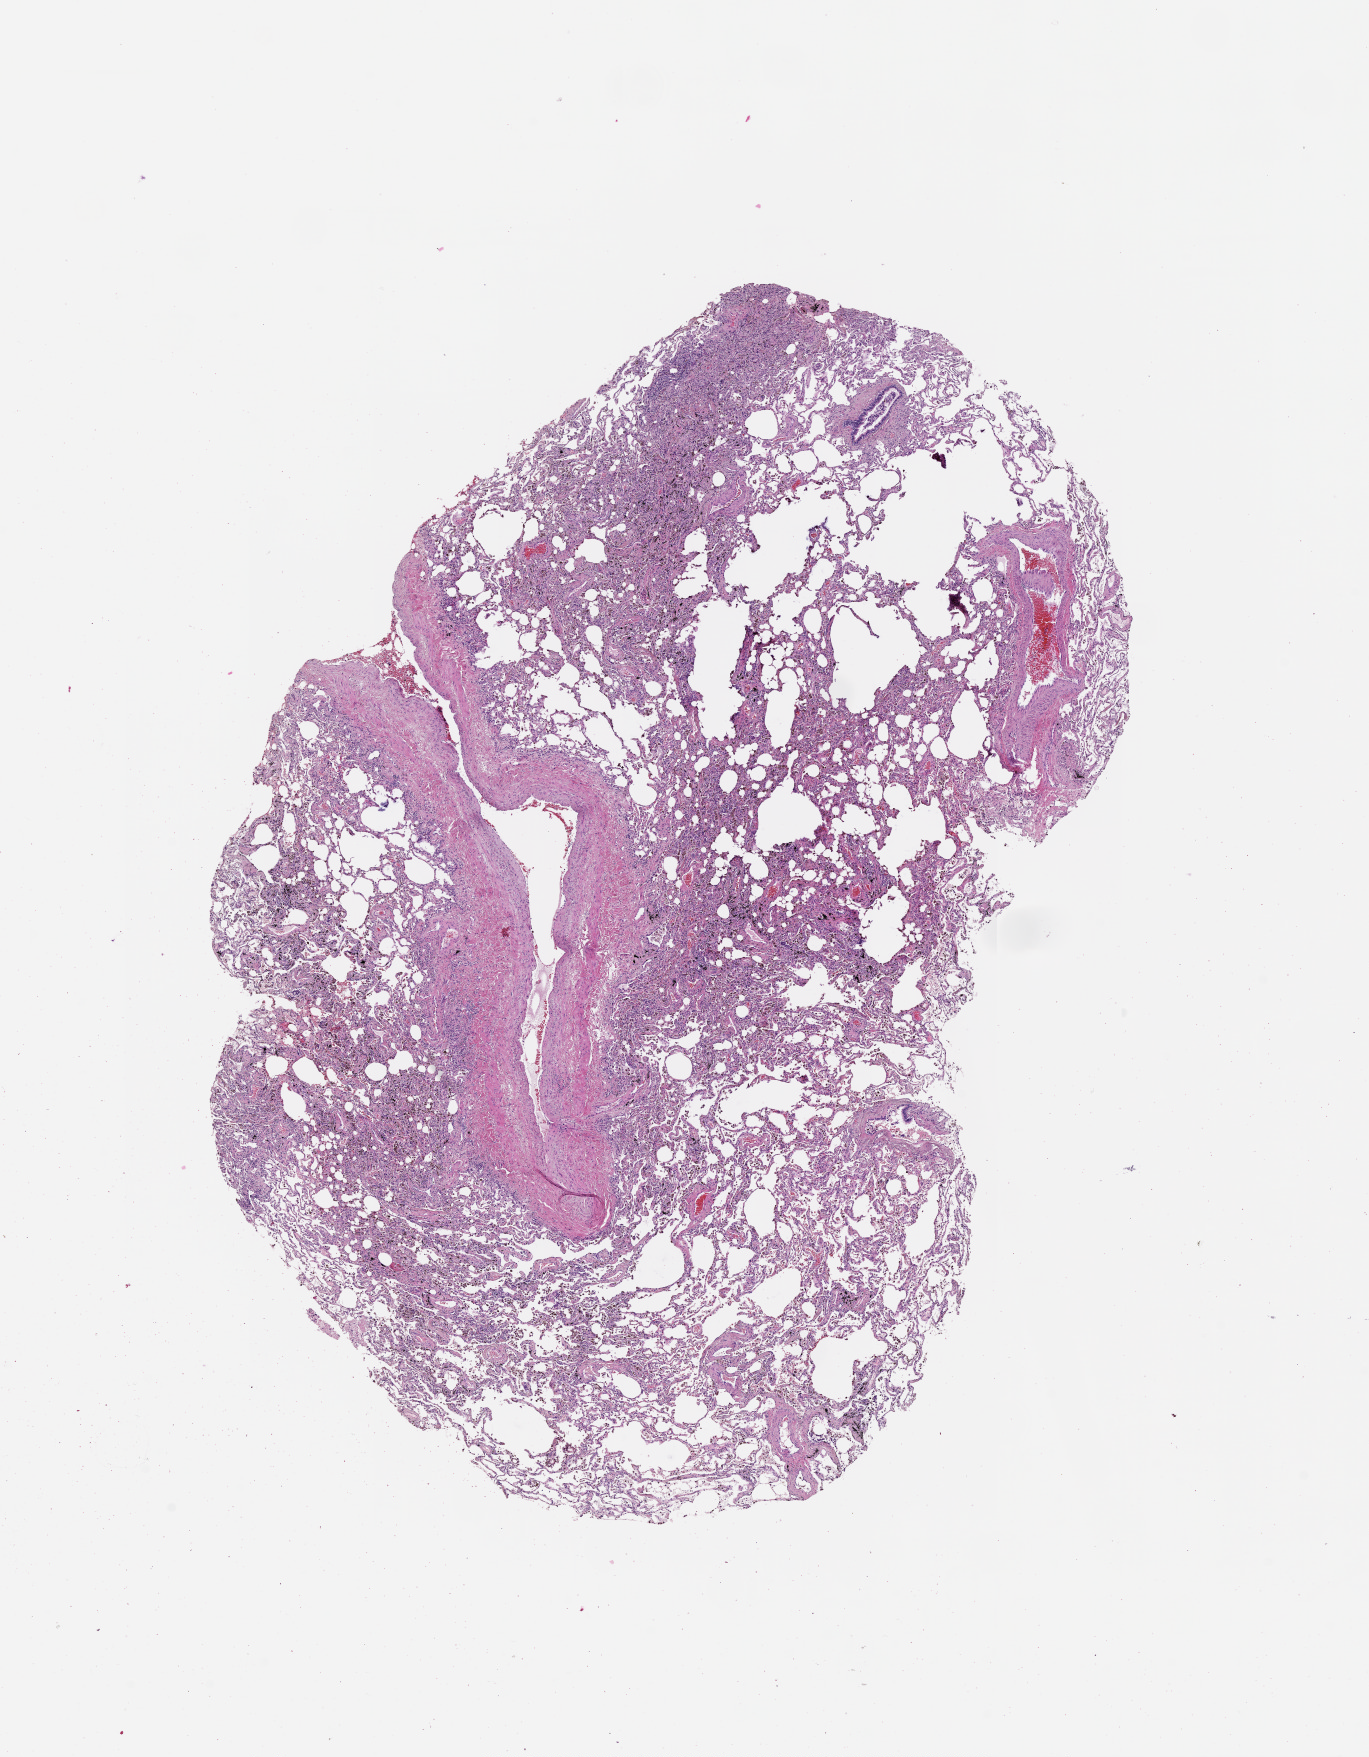
Whole-slide histology image, Hematoxylin and eosin (H&E) stained — a low-resolution overview of the entire scanned area, about 11.0 x 14.1 mm (from a 20x scan). Lung, normal (non-tumour) tissue. Patient: male, age 60 years.
This section: normal (non-tumour) tissue from the same patient. Patient diagnosis (cohort enrolment): squamous cell carcinoma (lung).